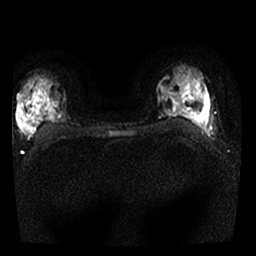
Breast MRI, one axial slice. Position 14 of 25 along the scan axis. Diffusion-weighted series; image 2 of 4 stored at this slice position (different b-values; order by instance number). 1.5 T. 4 mm slice thickness. 256 × 256 image matrix, field of view 300 × 300 mm. Female patient.
Annotated regions visible in this slice (manually delineated by an expert):
- tumour on diffusion-weighted imaging: box from (x=20, y=113) to (x=28, y=125) px